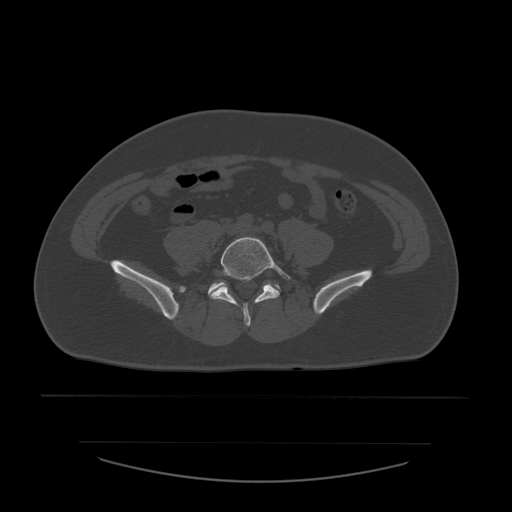
CT including the spine, one axial slice. Slice 117 of 532 in the series (ordered by position). 120 kVp. Bone window (W 1800 / L 400 HU). 1.25 mm slice thickness. 512 × 512 image matrix, field of view 441 × 441 mm. Patient age 44 years. Case-level facts recorded for this patient, not image findings: primary cancer: soft tissue sarcoma.
Outlined on this slice (semi-automatic segmentation, software-assisted and operator-edited):
- L5 vertebra: bounding box (x1, y1, x2, y2) in pixels: (210, 237, 291, 327)